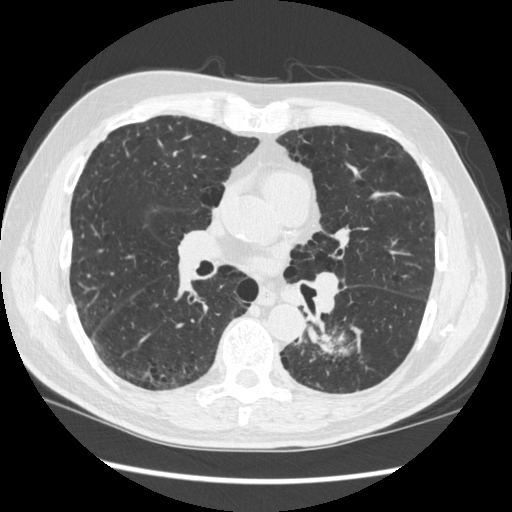
Low-dose screening chest CT, one axial slice. Position 169 of 348 along the scan axis. Reconstruction kernel STANDARD. Lung window (W 1500 / L -600 HU). 1.25 mm slice thickness. 512 × 512 image matrix.
Outlined on this slice (manually delineated by an expert):
- lesion 1 (tumor, lower lobe of left lung): box from (x=317, y=334) to (x=350, y=360) px